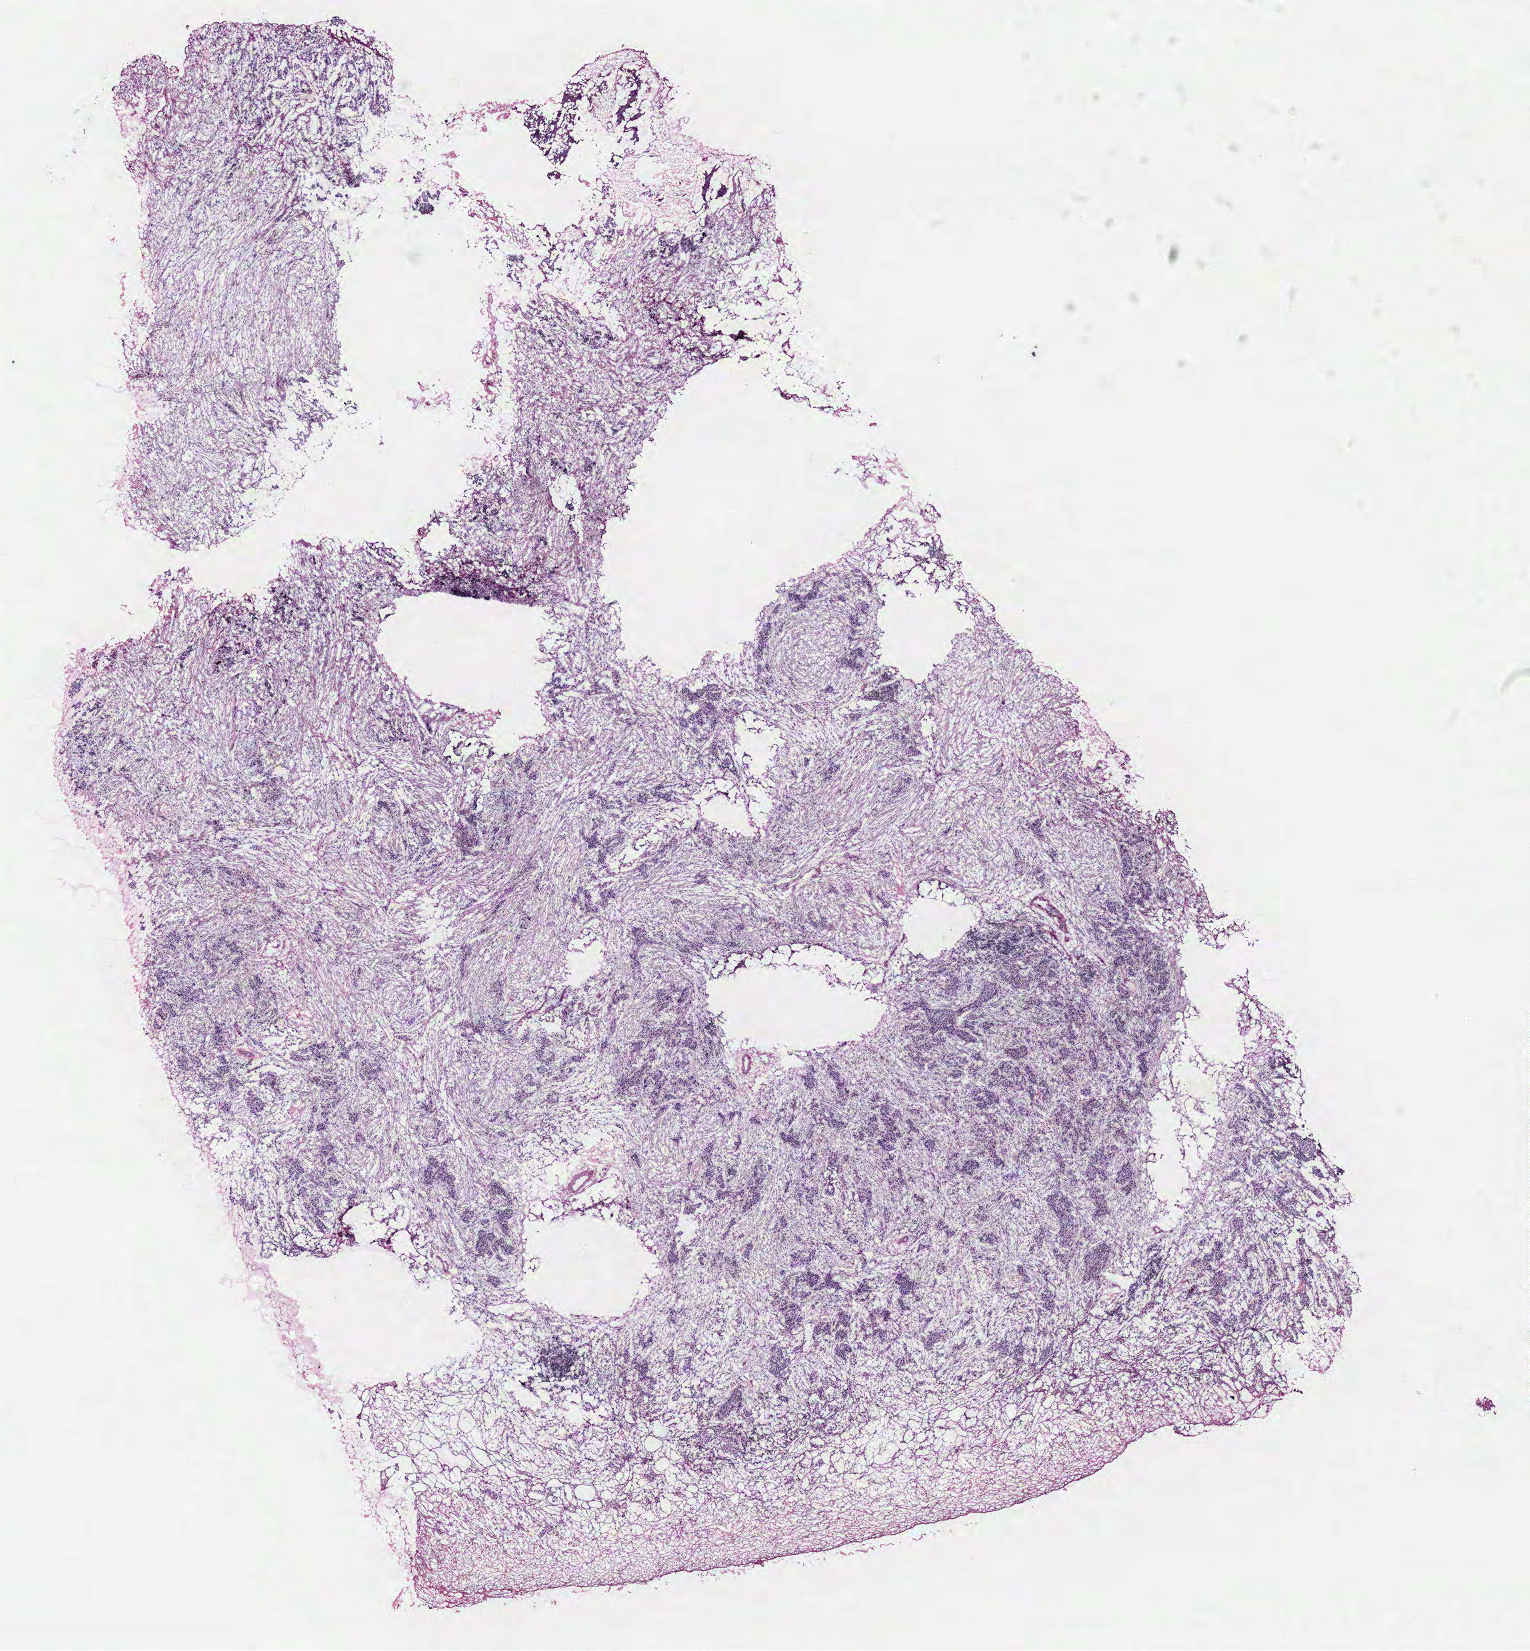
Digitized Hematoxylin and eosin (H&E) stained tissue section (whole slide), a low-resolution overview of the entire scanned area, about 12.2 x 13.2 mm (slide scanned at 40x). Tumour tissue sample, ovary. Female, 58 y/o.
Diagnosis: Serous adenocarcinoma, NOS (fallopian tube).